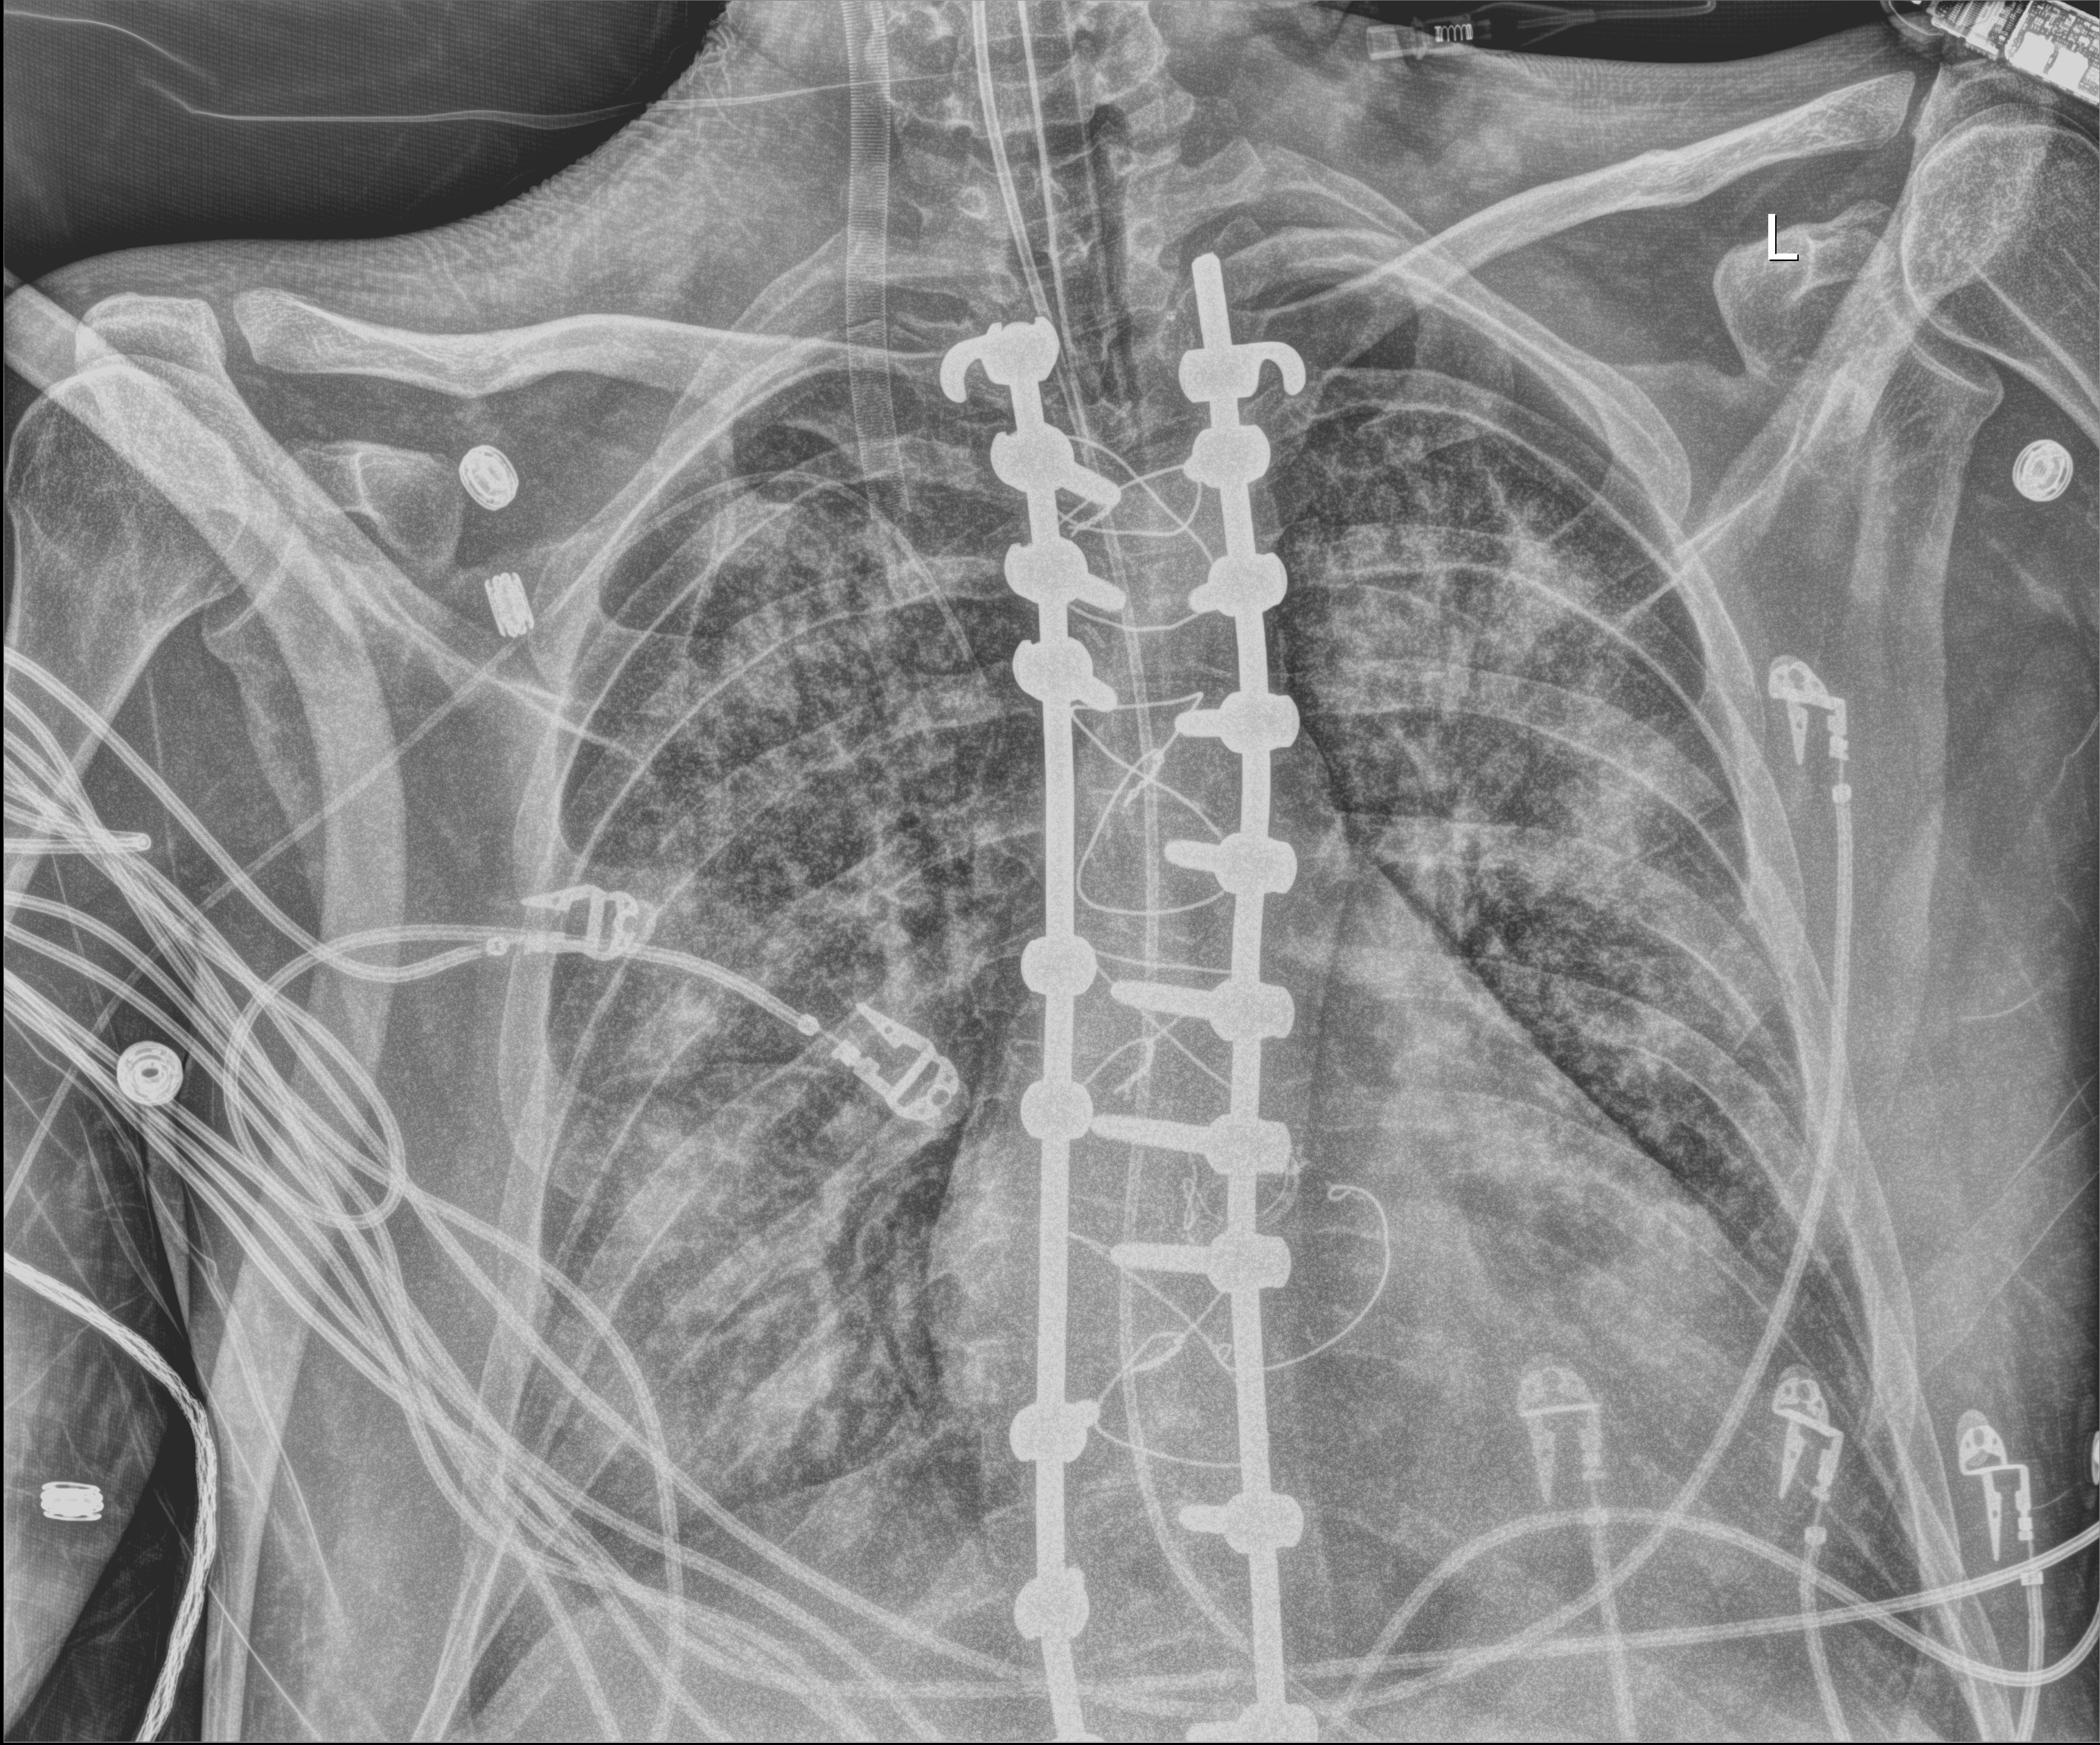
Chest X-ray (portable); anteroposterior (AP) projection. Adult patient hospitalised with COVID-19, age 18–59 years.
Admission-level facts for this patient (not findings on this image; timing relative to this image not recorded): COPD (admission record): no; mechanically ventilated during this hospital stay: yes.